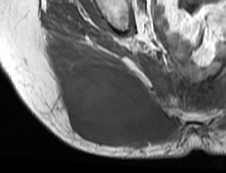
MRI of an extremity soft-tissue mass, one axial slice; position 39 of 73 along the scan axis; MR volume resampled by the dataset authors to the PET/CT grid (not the native acquisition matrix); 226 × 173 image matrix, field of view 221 × 169 mm. Female patient. From the clinical record (not read from this slice): histological type: spindle cell suggestive of myxofibrosarcoma; grade: intermediate; site of the primary tumour: right buttock.
Outlined on this slice (expert contour drawn on MRI and transferred to this co-registered scan by the dataset authors):
- gross tumour volume (mass): bounding box [x1, y1, x2, y2] px = [57, 61, 181, 148]